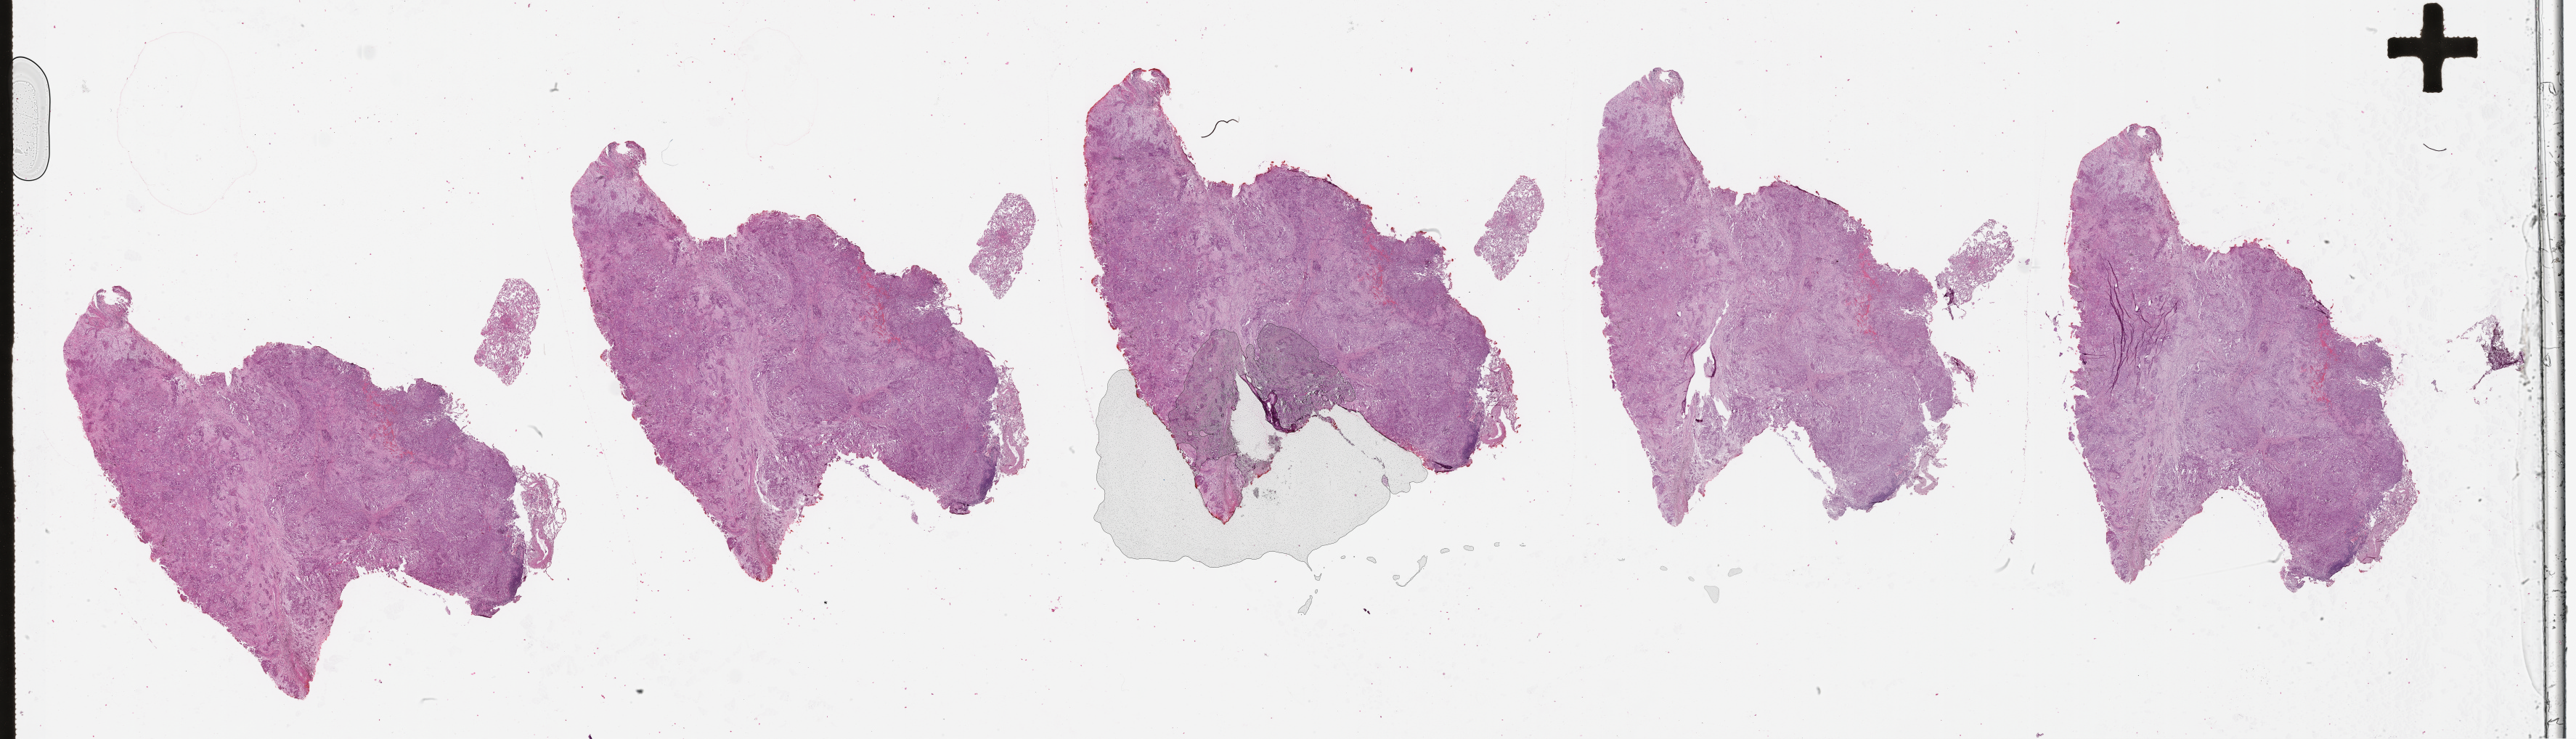
Whole-slide histology image, H&E, a low-resolution overview of the entire scanned area, about 57.1 x 16.4 mm (from a 20x scan), lung, tissue type not recorded.
Patient diagnosis (cohort enrolment): lung adenocarcinoma (lung).